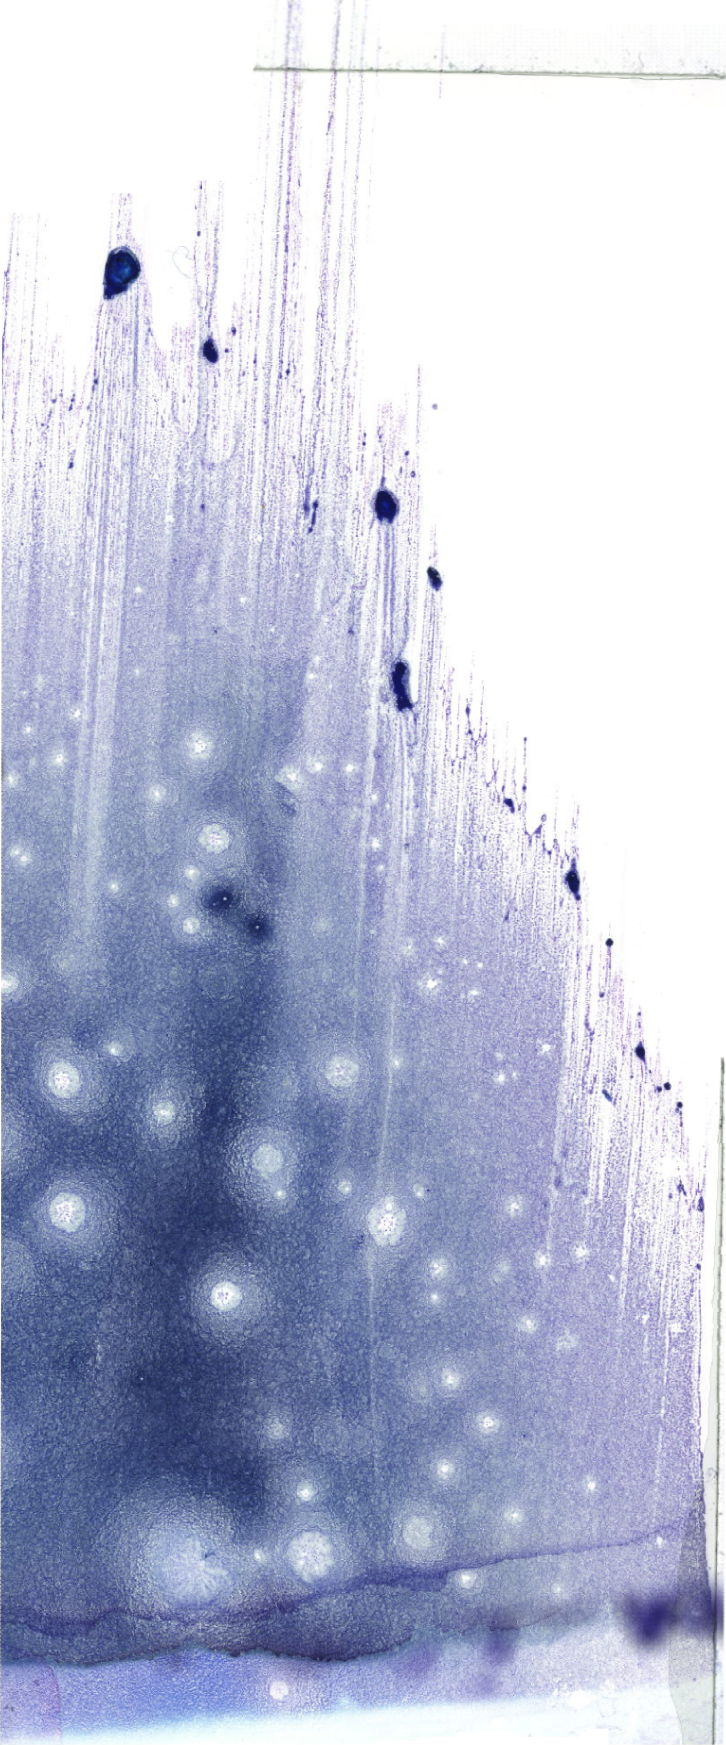
May-Grünwald–Giemsa-stained marrow aspirate smear (whole slide) — low-resolution overview of the scanned area, about 20.6 x 49.5 mm. Female patient.
- diagnosis: B Acute Lymphoblastic Leukemia